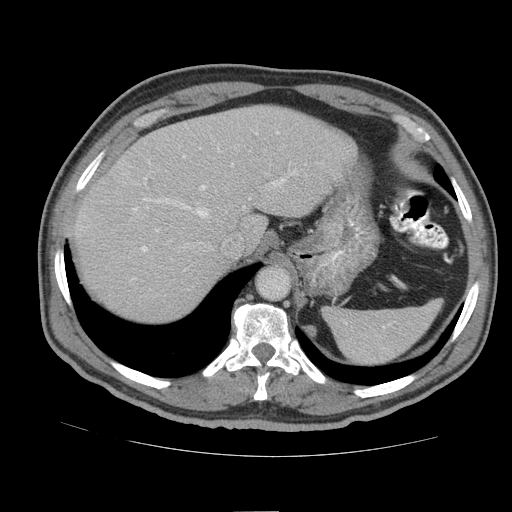
Contrast-enhanced abdominal CT (liver protocol), one axial slice; slice 67 of 105 in the series (ordered by position); reconstruction kernel STANDARD; 140 kVp; soft-tissue window (W 400 / L 40 HU); 512 × 512 image matrix, field of view 380 × 380 mm. Case-level facts recorded for this patient, not image findings: diagnosis: hepatocellular carcinoma (patient treated with transarterial chemoembolisation; whether this scan precedes or follows treatment is not stated here); TNM stage (as recorded): Stage-IIIB; Child-Pugh class: A; tumour nodularity: multinodular.
Annotated regions visible in this slice (semi-automatic segmentation, software-assisted and operator-edited):
- abdominal aorta: bounding box <258,268,289,298> (left, top, right, bottom; pixels)
- liver parenchyma outside the tumour (the mass and vessels are separate outlines, so this box may not span the whole liver): <70,106,356,320>
- liver vessels: <134,132,285,251>